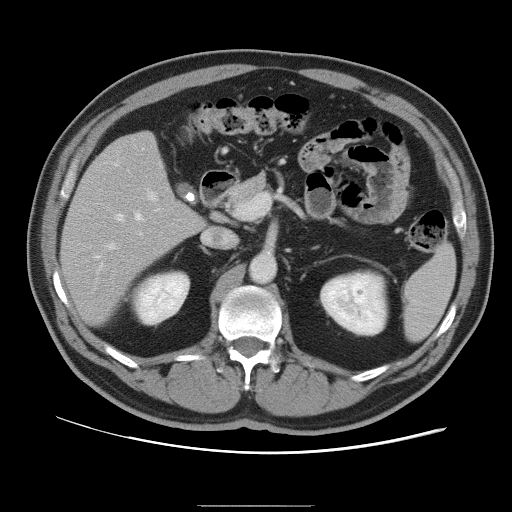
Contrast-enhanced abdominal CT, one axial slice; position 52 of 105 along the scan axis; intravenous contrast given; soft-tissue window (W 400 / L 40 HU); 5 mm slice thickness; 512 × 512 image matrix, field of view 399 × 399 mm. Male patient, age 64 years. Case-level facts recorded for this patient, not image findings: diagnosis: colorectal cancer liver metastases, imaged before liver resection; multiple liver metastases: yes; largest metastasis: 3 cm; disease in both lobes: yes.
Structures marked on this image (expert manual segmentation):
- hepatic veins: bounding box [x1, y1, x2, y2] px = [96, 213, 144, 270]
- liver: [63, 132, 203, 326]
- planned liver remnant (the part of the liver to remain after resection): [63, 132, 204, 326]
- portal vein (with intrahepatic branches): [106, 189, 157, 250]